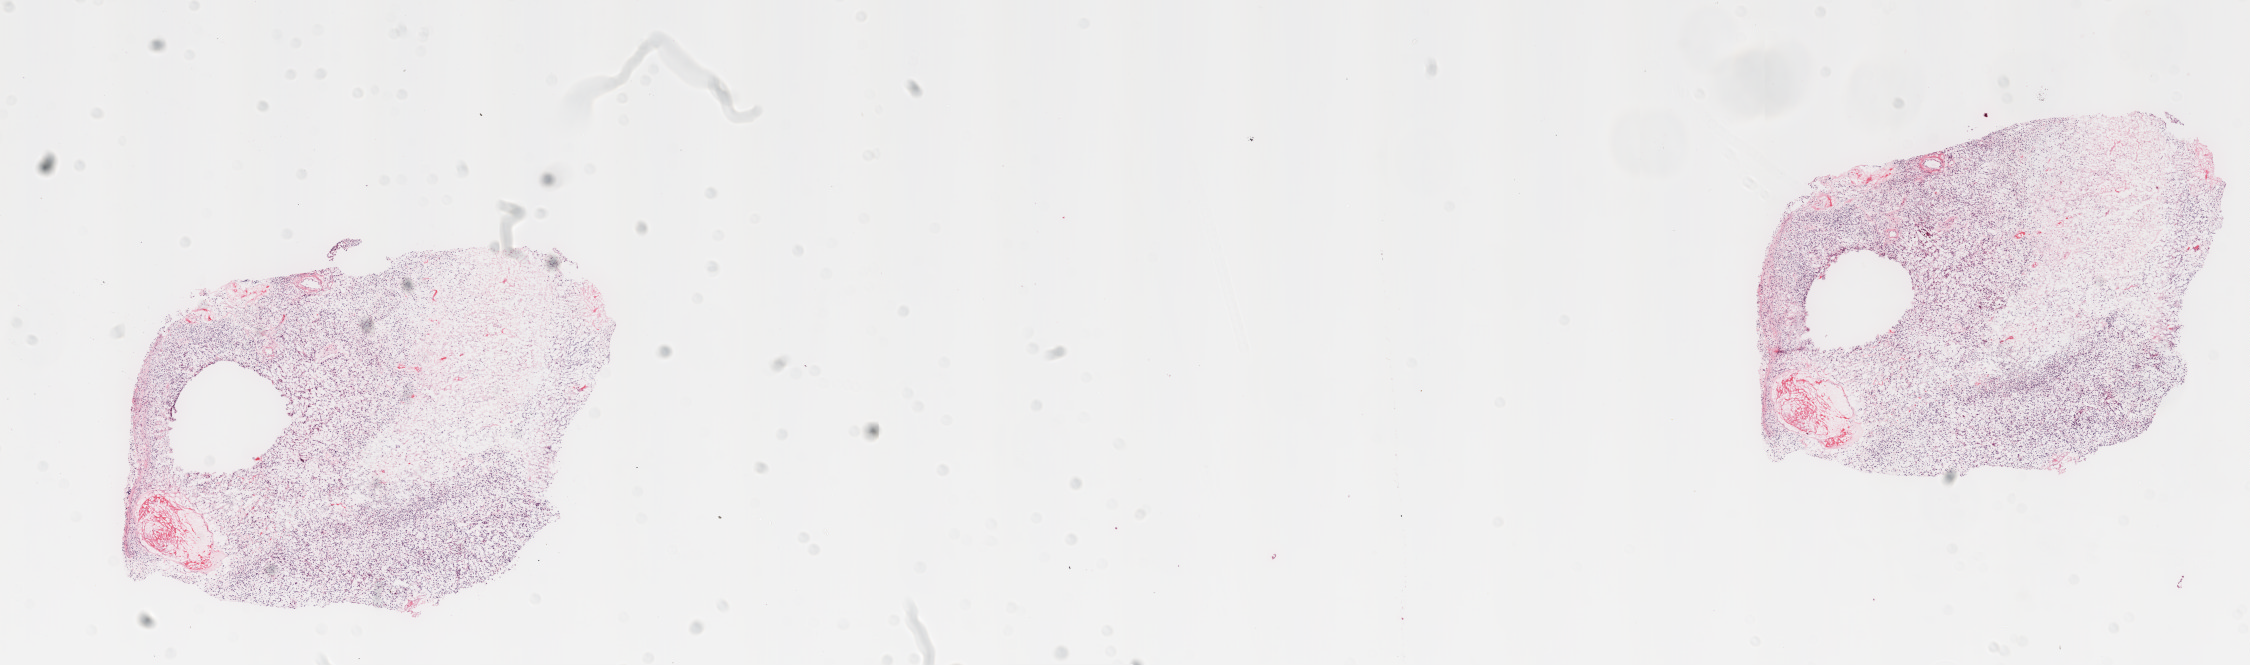
Digitized H&E tissue section (whole slide), shown as a low-resolution overview of the whole scanned area (about 18.1 x 5.3 mm, from a 20x scan), frozen section from the top of the tissue portion, primary tumour sample from the brain. Female patient; age at initial diagnosis 64 years. Composition of this section per pathologist review: tumour cells 60%, tumour nuclei 85%, normal cells 0%, stromal cells 5%, necrosis 35%.
Pathologic diagnosis: Glioblastoma.